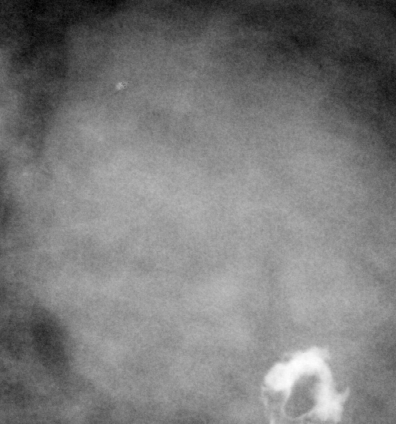
Crop from a digitized film mammogram around one marked abnormality; right breast; CC view; BI-RADS breast density category 2 (scale 1–4).
- Marked abnormality: mass, shape round, margins microlobulated; BI-RADS assessment category 4; subtlety rating 5 on a 1 (subtle) to 5 (obvious) scale; pathology (as recorded): benign.